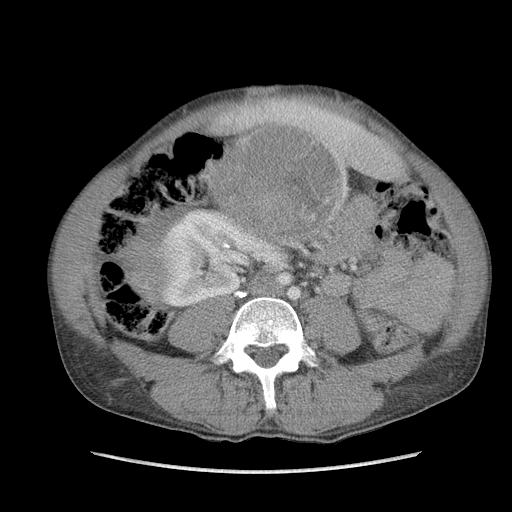
Contrast-enhanced abdominal CT, one axial slice. Slice 42 of 115 in the series (ordered by position). Soft-tissue window (W 400 / L 40 HU). 5 mm slice thickness. 512 × 512 image matrix, field of view 360 × 360 mm. Male patient. From the clinical record (not read from this slice): diagnosis: adrenocortical carcinoma; tumour side: right adrenal; Ki-67 index: 13 %; stage (as recorded): 3.
Annotated regions visible in this slice (semi-automatic segmentation, software-assisted and operator-edited):
- mass: bounding box [x1, y1, x2, y2] px = [127, 126, 336, 298]